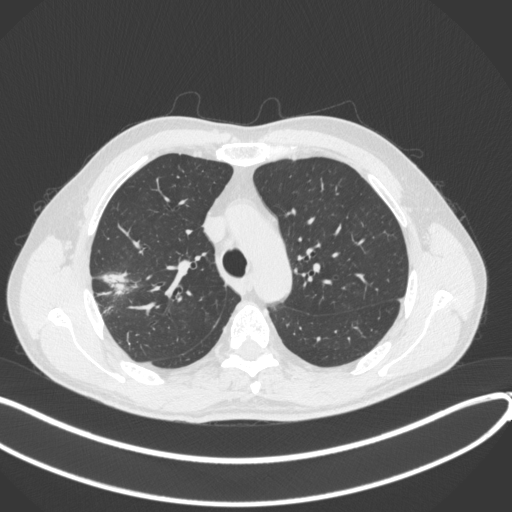
Chest CT, one axial slice. Position 305 of 381 along the scan axis. Reconstruction kernel B31f. 120 kVp. Lung window (W 1500 / L -600 HU). 1 mm slice thickness. 512 × 512 image matrix, field of view 400 × 400 mm. Male patient, age 62 years. Case-level facts recorded for this patient, not image findings: clinical TNM (as recorded): T1c N0 M0; histopathological grade: G2-3.
Annotated regions visible in this slice (rectangle marked by the reading radiologist):
- lung tumour (recorded histology: adenocarcinoma): bounding box [x1, y1, x2, y2] px = [100, 265, 139, 302]